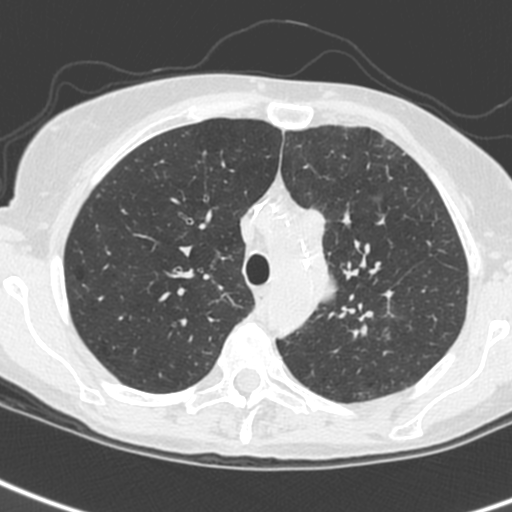
Low-dose screening chest CT, one axial slice; slice 186 of 242 in the series (ordered by position); 120 kVp; lung window (W 1500 / L -600 HU); 1.3 mm slice thickness; 512 × 512 image matrix.
Outlined on this slice (manually delineated by an expert):
- lesion 3 (tumor, upper lobe of left lung): bounding box [x1, y1, x2, y2] px = [302, 208, 336, 303]